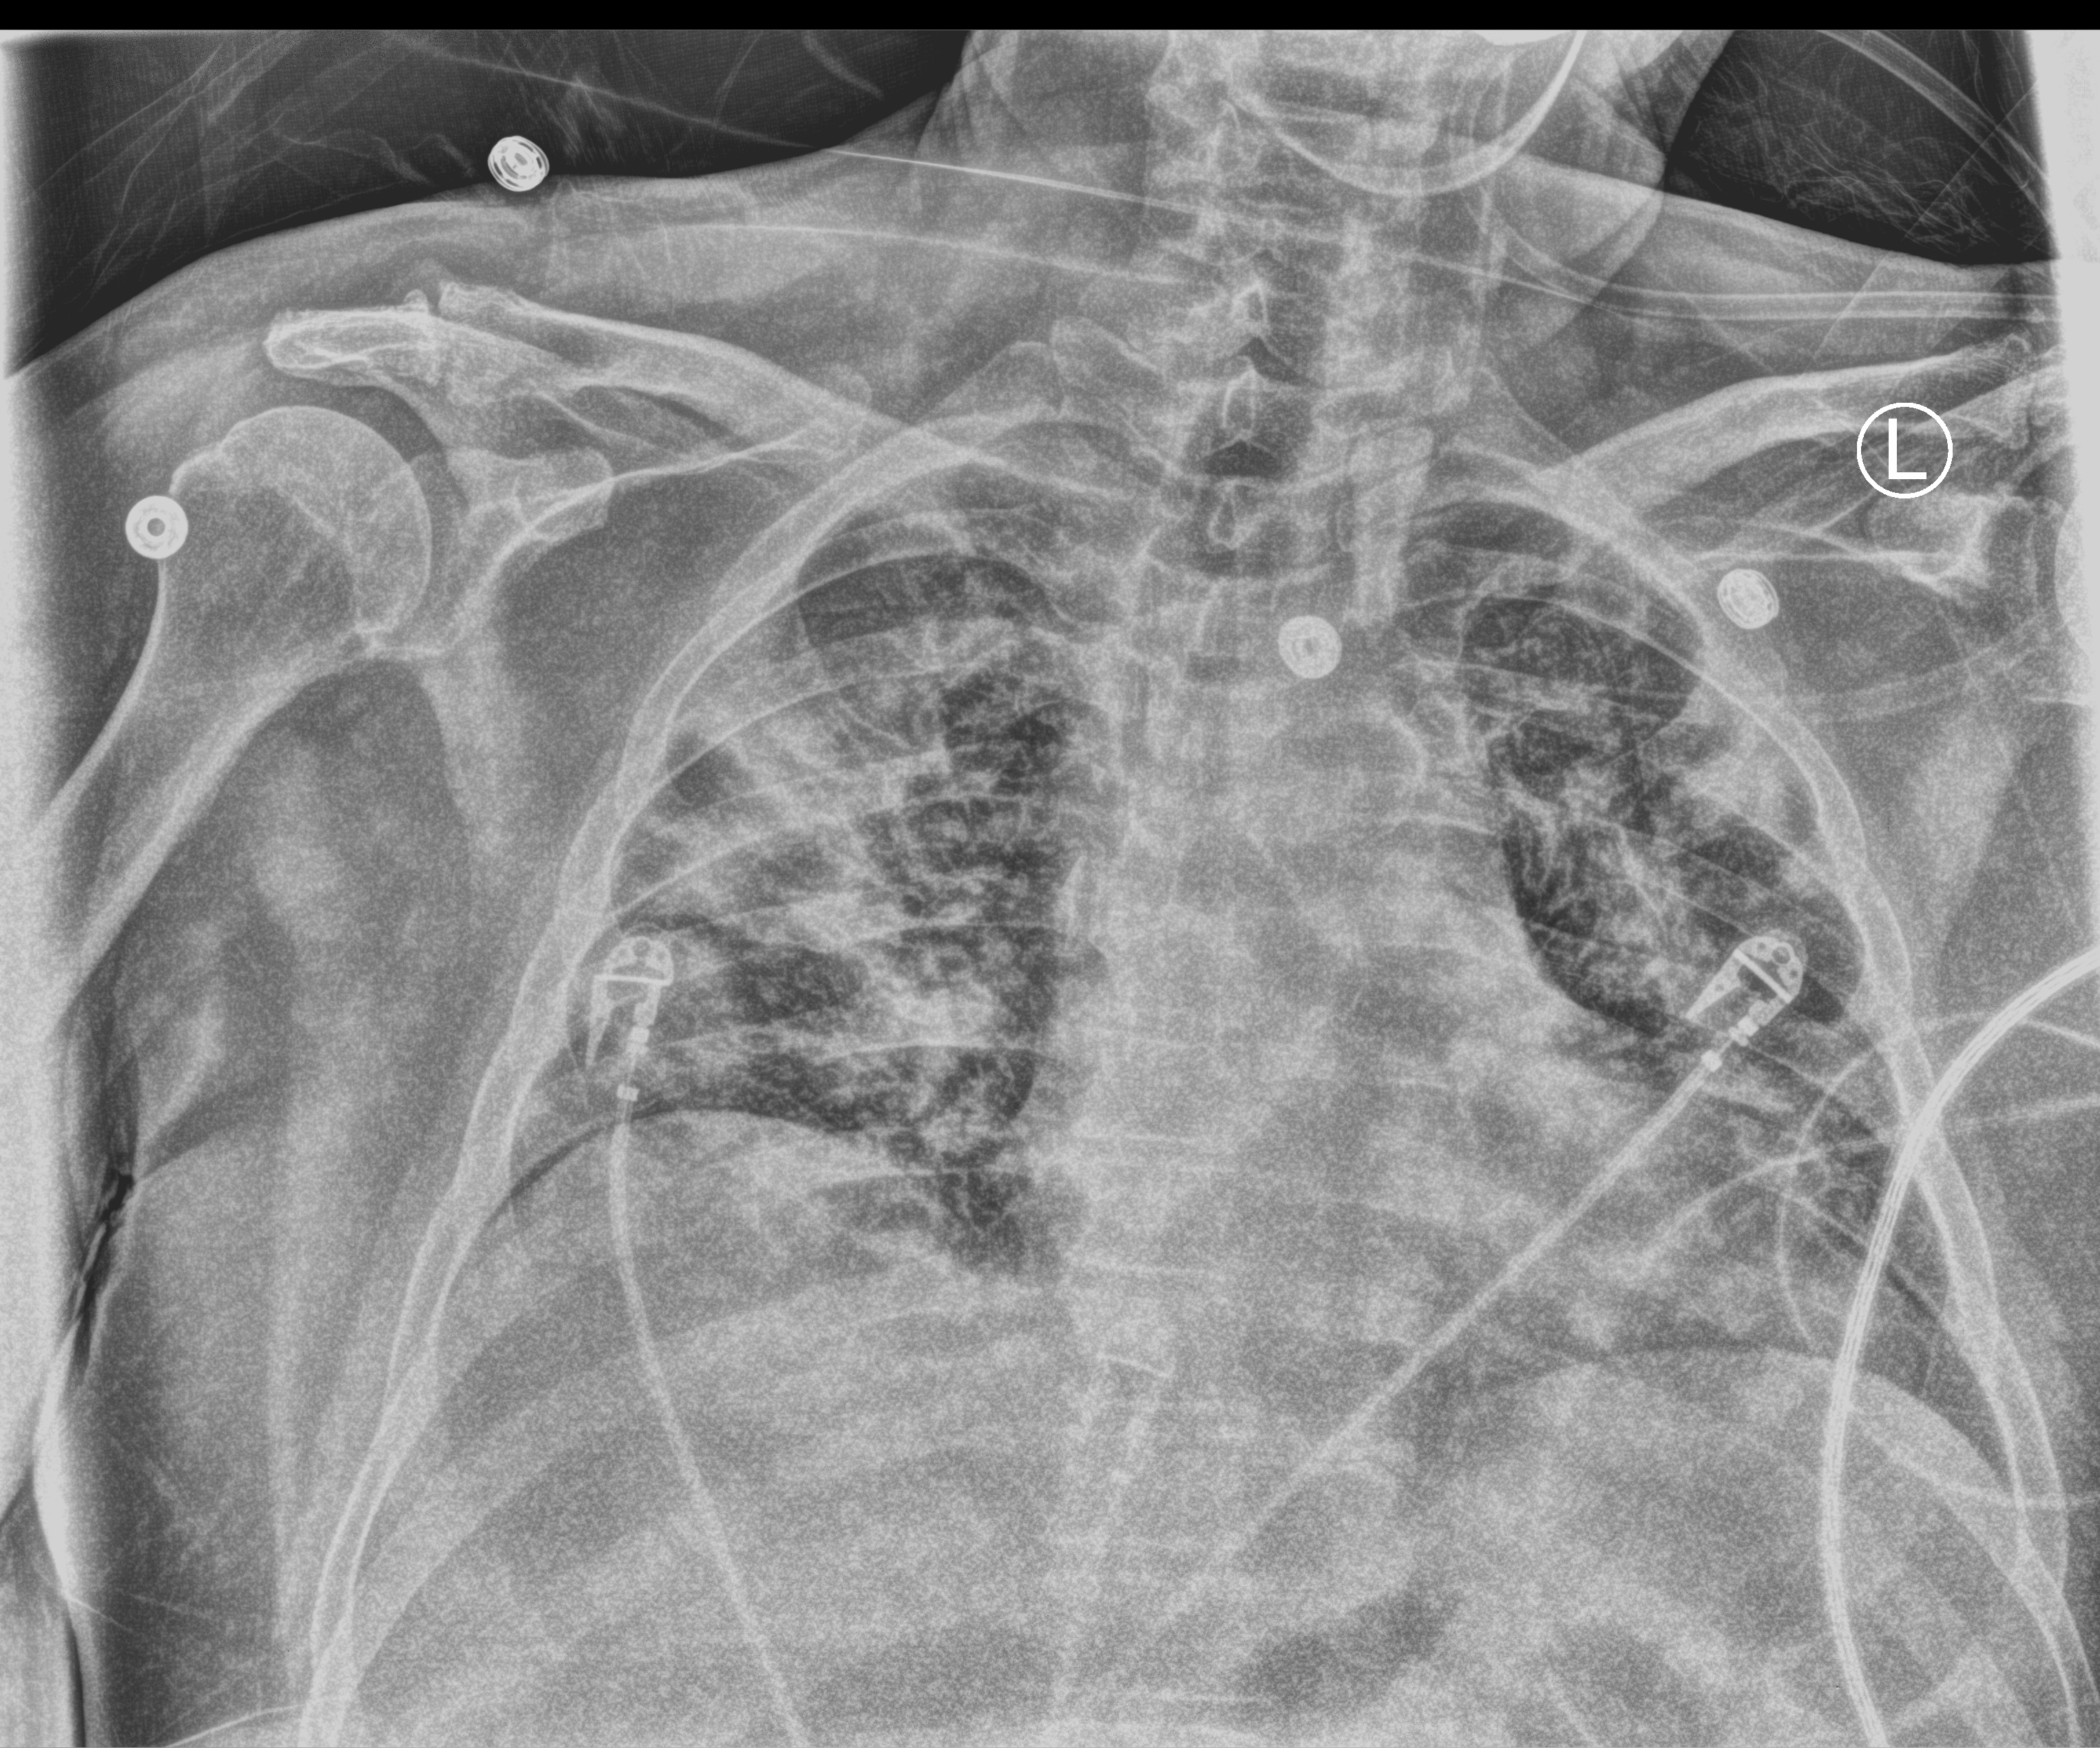
Chest X-ray (portable); anteroposterior (AP) projection. Male patient hospitalised with COVID-19, age 60–74 years.
From the hospital-stay record, not from the radiograph (when in the stay this image was taken is not recorded):
- COPD (admission record): no